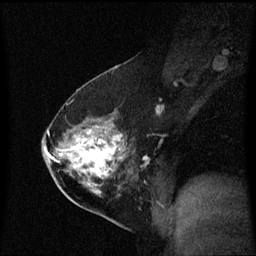
Breast MRI (dynamic contrast-enhanced), one sagittal slice. Position 34 of 60 along the scan axis. Dynamic contrast-enhanced series, image 2 of 3 at this slice position (ordered by acquisition). 1.5 T. TE 4.2 ms, TR 8.4 ms. 2 mm slice thickness. 256 × 256 image matrix, field of view 210 × 210 mm. Female patient, age 54 years. From the clinical record (not read from this slice): setting: breast cancer imaged before/during neoadjuvant chemotherapy; receptor status: HER2-positive.
Outlined on this slice (semi-automatically segmented with operator editing):
- analysis volume of interest (the breast-tissue region the enhancement analysis was run in; not a lesion): box from (x=59, y=115) to (x=141, y=199) px
- tumour enhancement mask (voxels above the 70 % enhancement threshold inside the analysis volume of interest): (x=70, y=128)–(x=124, y=188)